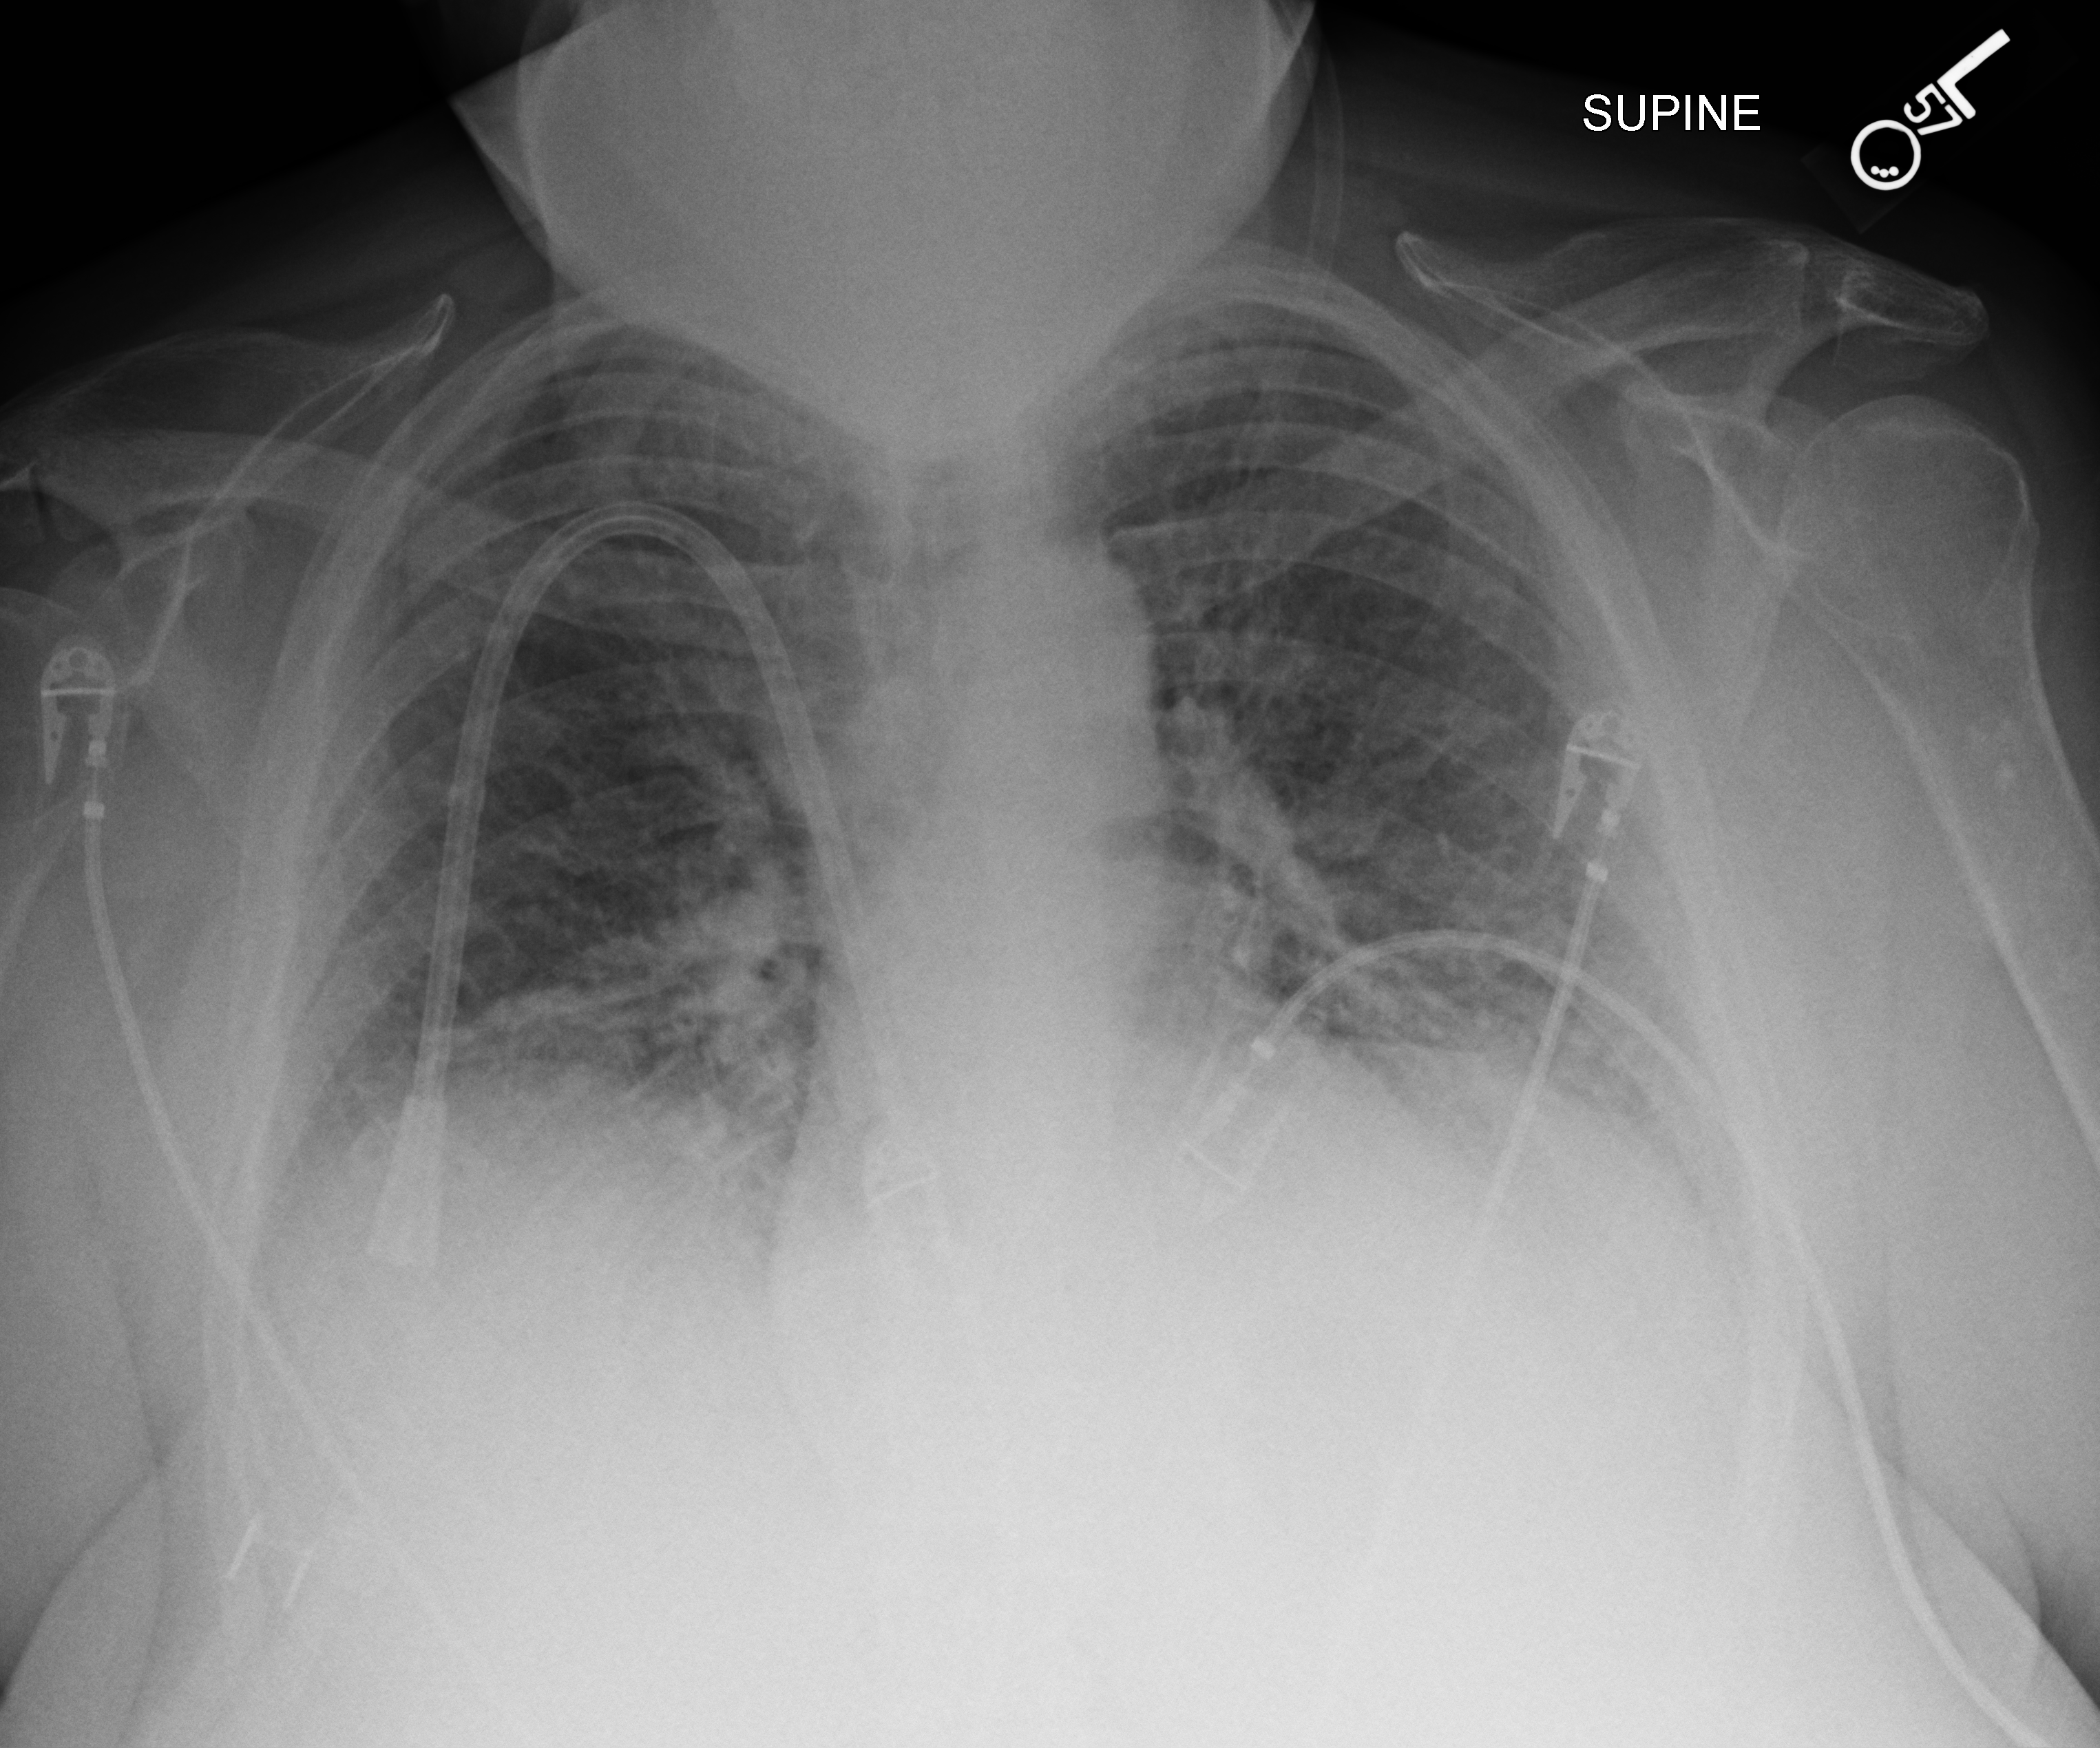
Bedside chest radiograph (computed radiography); anteroposterior (AP) projection. Patient hospitalised with COVID-19; female, aged 60–74 years.
Hospital-stay facts (about this admission, not read from this image; timing relative to this image not recorded): admitted to intensive care during this hospital stay: no; mechanically ventilated during this hospital stay: no.